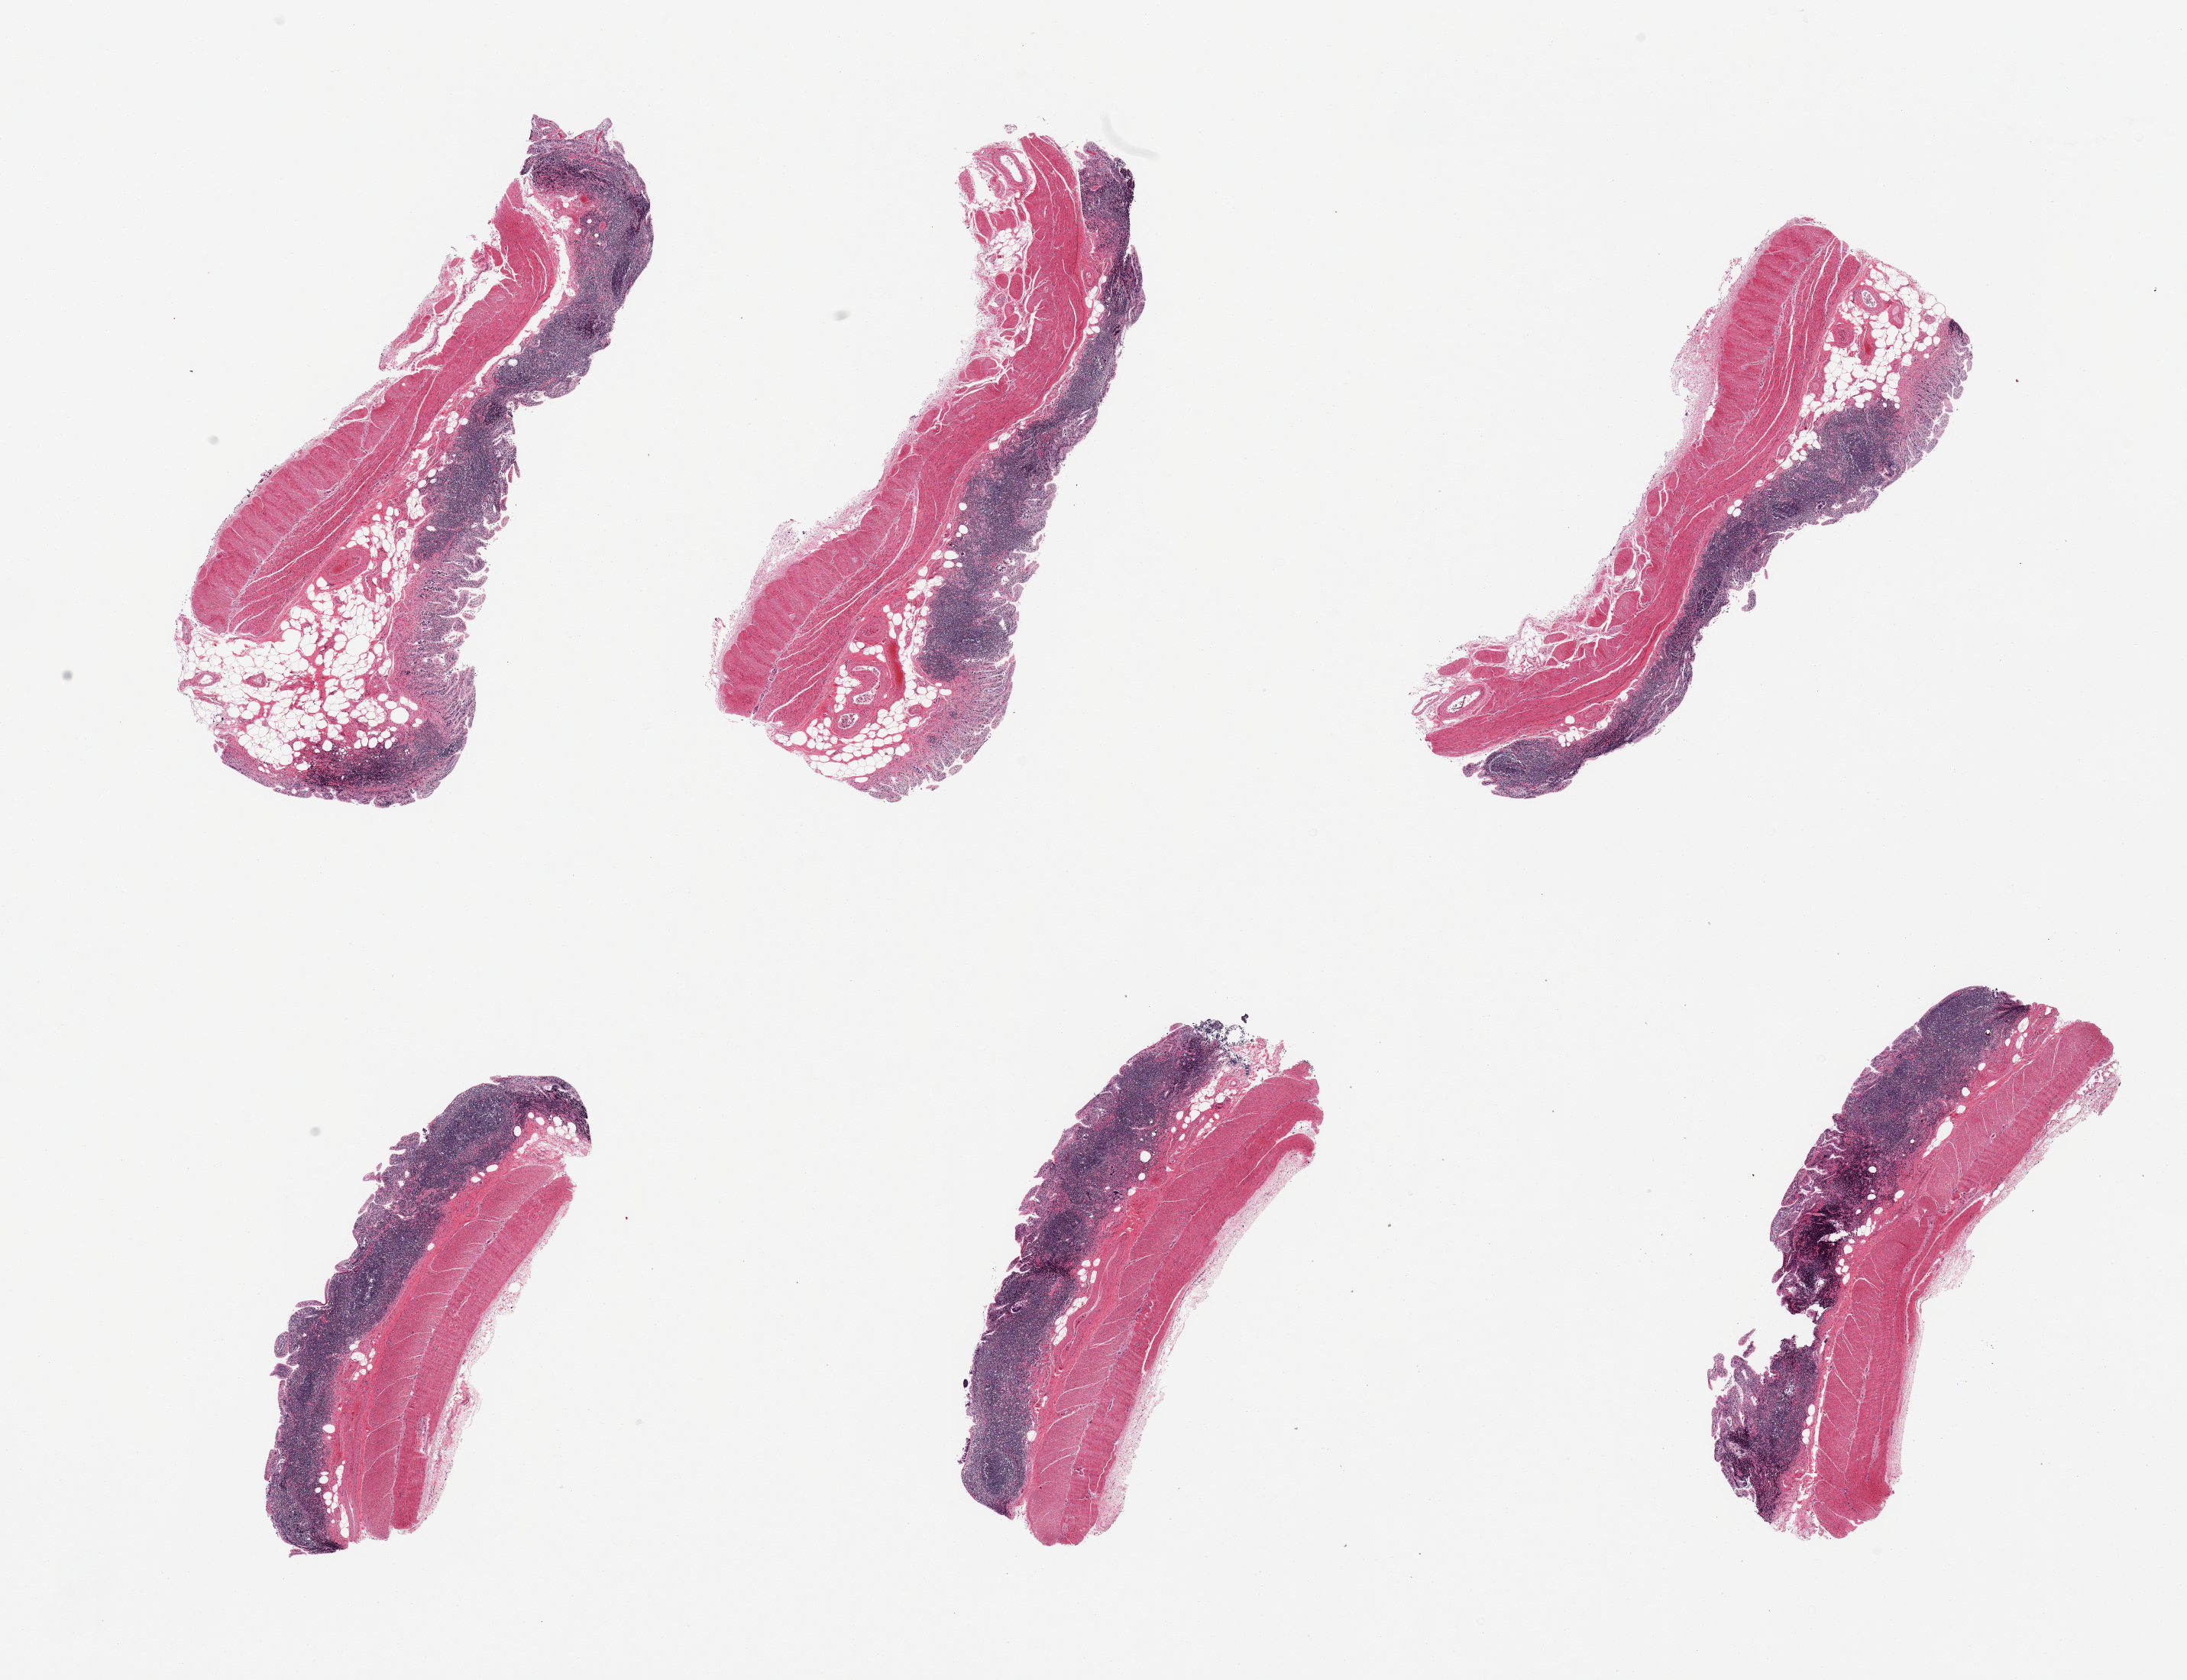
Whole-slide image, H&E stain — low-resolution overview of the scanned area, about 22.6 x 17.4 mm (acquisition: 20x scan). Male donor.
Specimen: PAXgene-fixed paraffin-embedded (PFPE) section; sampled site (target tissue): ileum; donor tissue sample.